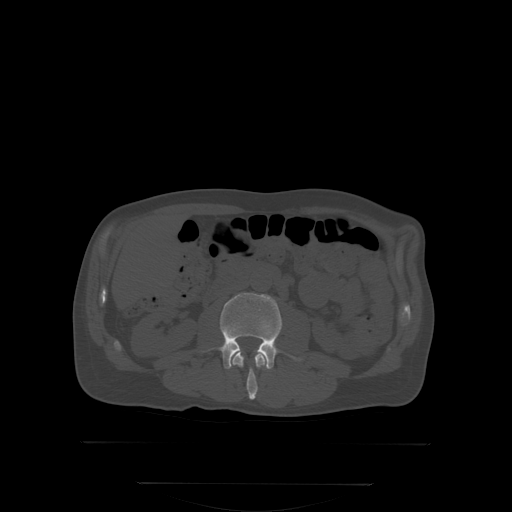
CT including the spine, one axial slice; slice 128 of 350 in the series (ordered by position); bone window (W 1800 / L 400 HU); 2.5 mm slice thickness; 512 × 512 image matrix, field of view 500 × 500 mm. Patient: male, 58 years. Case-level facts recorded for this patient, not image findings: primary cancer: prostate.
Outlined on this slice (semi-automatic segmentation, software-assisted and operator-edited):
- L2 vertebra: bounding box [x1, y1, x2, y2] px = [231, 350, 267, 400]
- L3 vertebra: [202, 293, 305, 369]